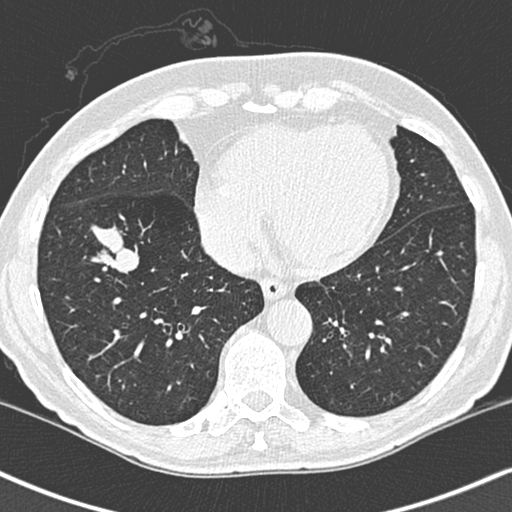
Low-dose screening chest CT, one axial slice. 120 kVp. Lung window (W 1500 / L -600 HU). 1.3 mm slice thickness. 512 × 512 image matrix, field of view 323 × 323 mm.
Annotated regions visible in this slice (manually delineated by an expert):
- lesion 1 (tumor, lower lobe of right lung): bounding box (x1, y1, x2, y2) in pixels: (91, 187, 139, 235)